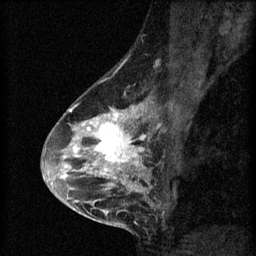
Breast MRI (dynamic contrast-enhanced), one sagittal slice; position 37 of 60 along the scan axis; 3 images stored at this slice position (order not interpretable as contrast timing); 1.5 T; TE 4.2 ms, TR 8.2 ms; 2 mm slice thickness; 256 × 256 image matrix, field of view 180 × 180 mm. Female patient, age 45 years.
Outlined on this slice (semi-automatically segmented with operator editing):
- analysis volume of interest (the breast-tissue region the enhancement analysis was run in; not a lesion): box from (x=54, y=104) to (x=157, y=217) px
- tumour enhancement mask (voxels above the 70 % enhancement threshold inside the analysis volume of interest): (x=56, y=104)–(x=153, y=211)